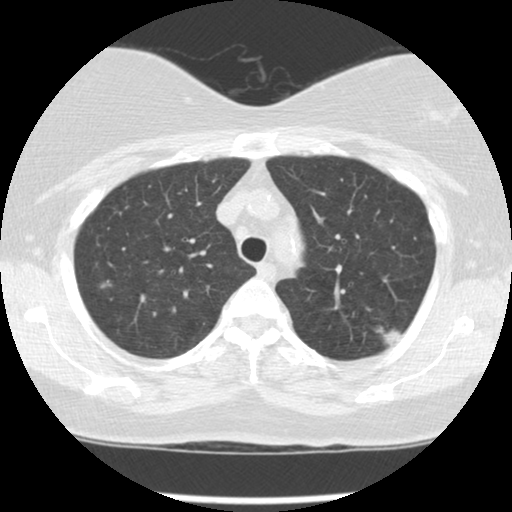
Low-dose screening chest CT, one axial slice. Position 102 of 127 along the scan axis. Reconstruction kernel STANDARD. 120 kVp. Lung window (W 1500 / L -600 HU). 2.5 mm slice thickness. 512 × 512 image matrix, field of view 310 × 310 mm.
Outlined on this slice (outlined manually by an expert reader):
- lesion 1 (tumor, upper lobe of left lung): bounding box <374,324,403,346> (left, top, right, bottom; pixels)